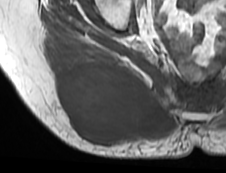
MRI of an extremity soft-tissue mass, one axial slice; slice 37 of 73 in the series (ordered by position); MR volume resampled by the dataset authors to the PET/CT grid (not the native acquisition matrix); 3.27 mm slice thickness; 226 × 173 image matrix. Female patient. From the clinical record (not read from this slice): histological type: spindle cell suggestive of myxofibrosarcoma; grade: intermediate; site of the primary tumour: right buttock.
Annotated regions visible in this slice (expert contour drawn on MRI and transferred to this co-registered scan by the dataset authors):
- gross tumour volume (mass): bounding box [x1, y1, x2, y2] px = [54, 58, 171, 144]